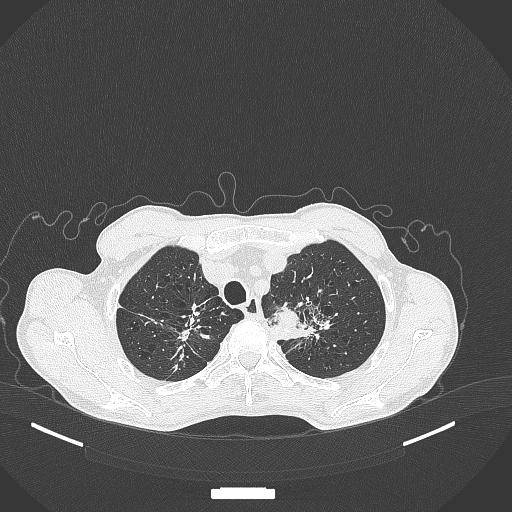
Chest CT, one axial slice. Reconstruction kernel B70f. Lung window (W 1500 / L -600 HU). 512 × 512 image matrix, field of view 400 × 400 mm. Male patient, age 65 years. From the clinical record (not read from this slice): clinical TNM (as recorded): T2b N0 M0.
Structures marked on this image (rectangle marked by the reading radiologist):
- lung tumour (recorded histology: adenocarcinoma): box from (x=270, y=300) to (x=302, y=332) px